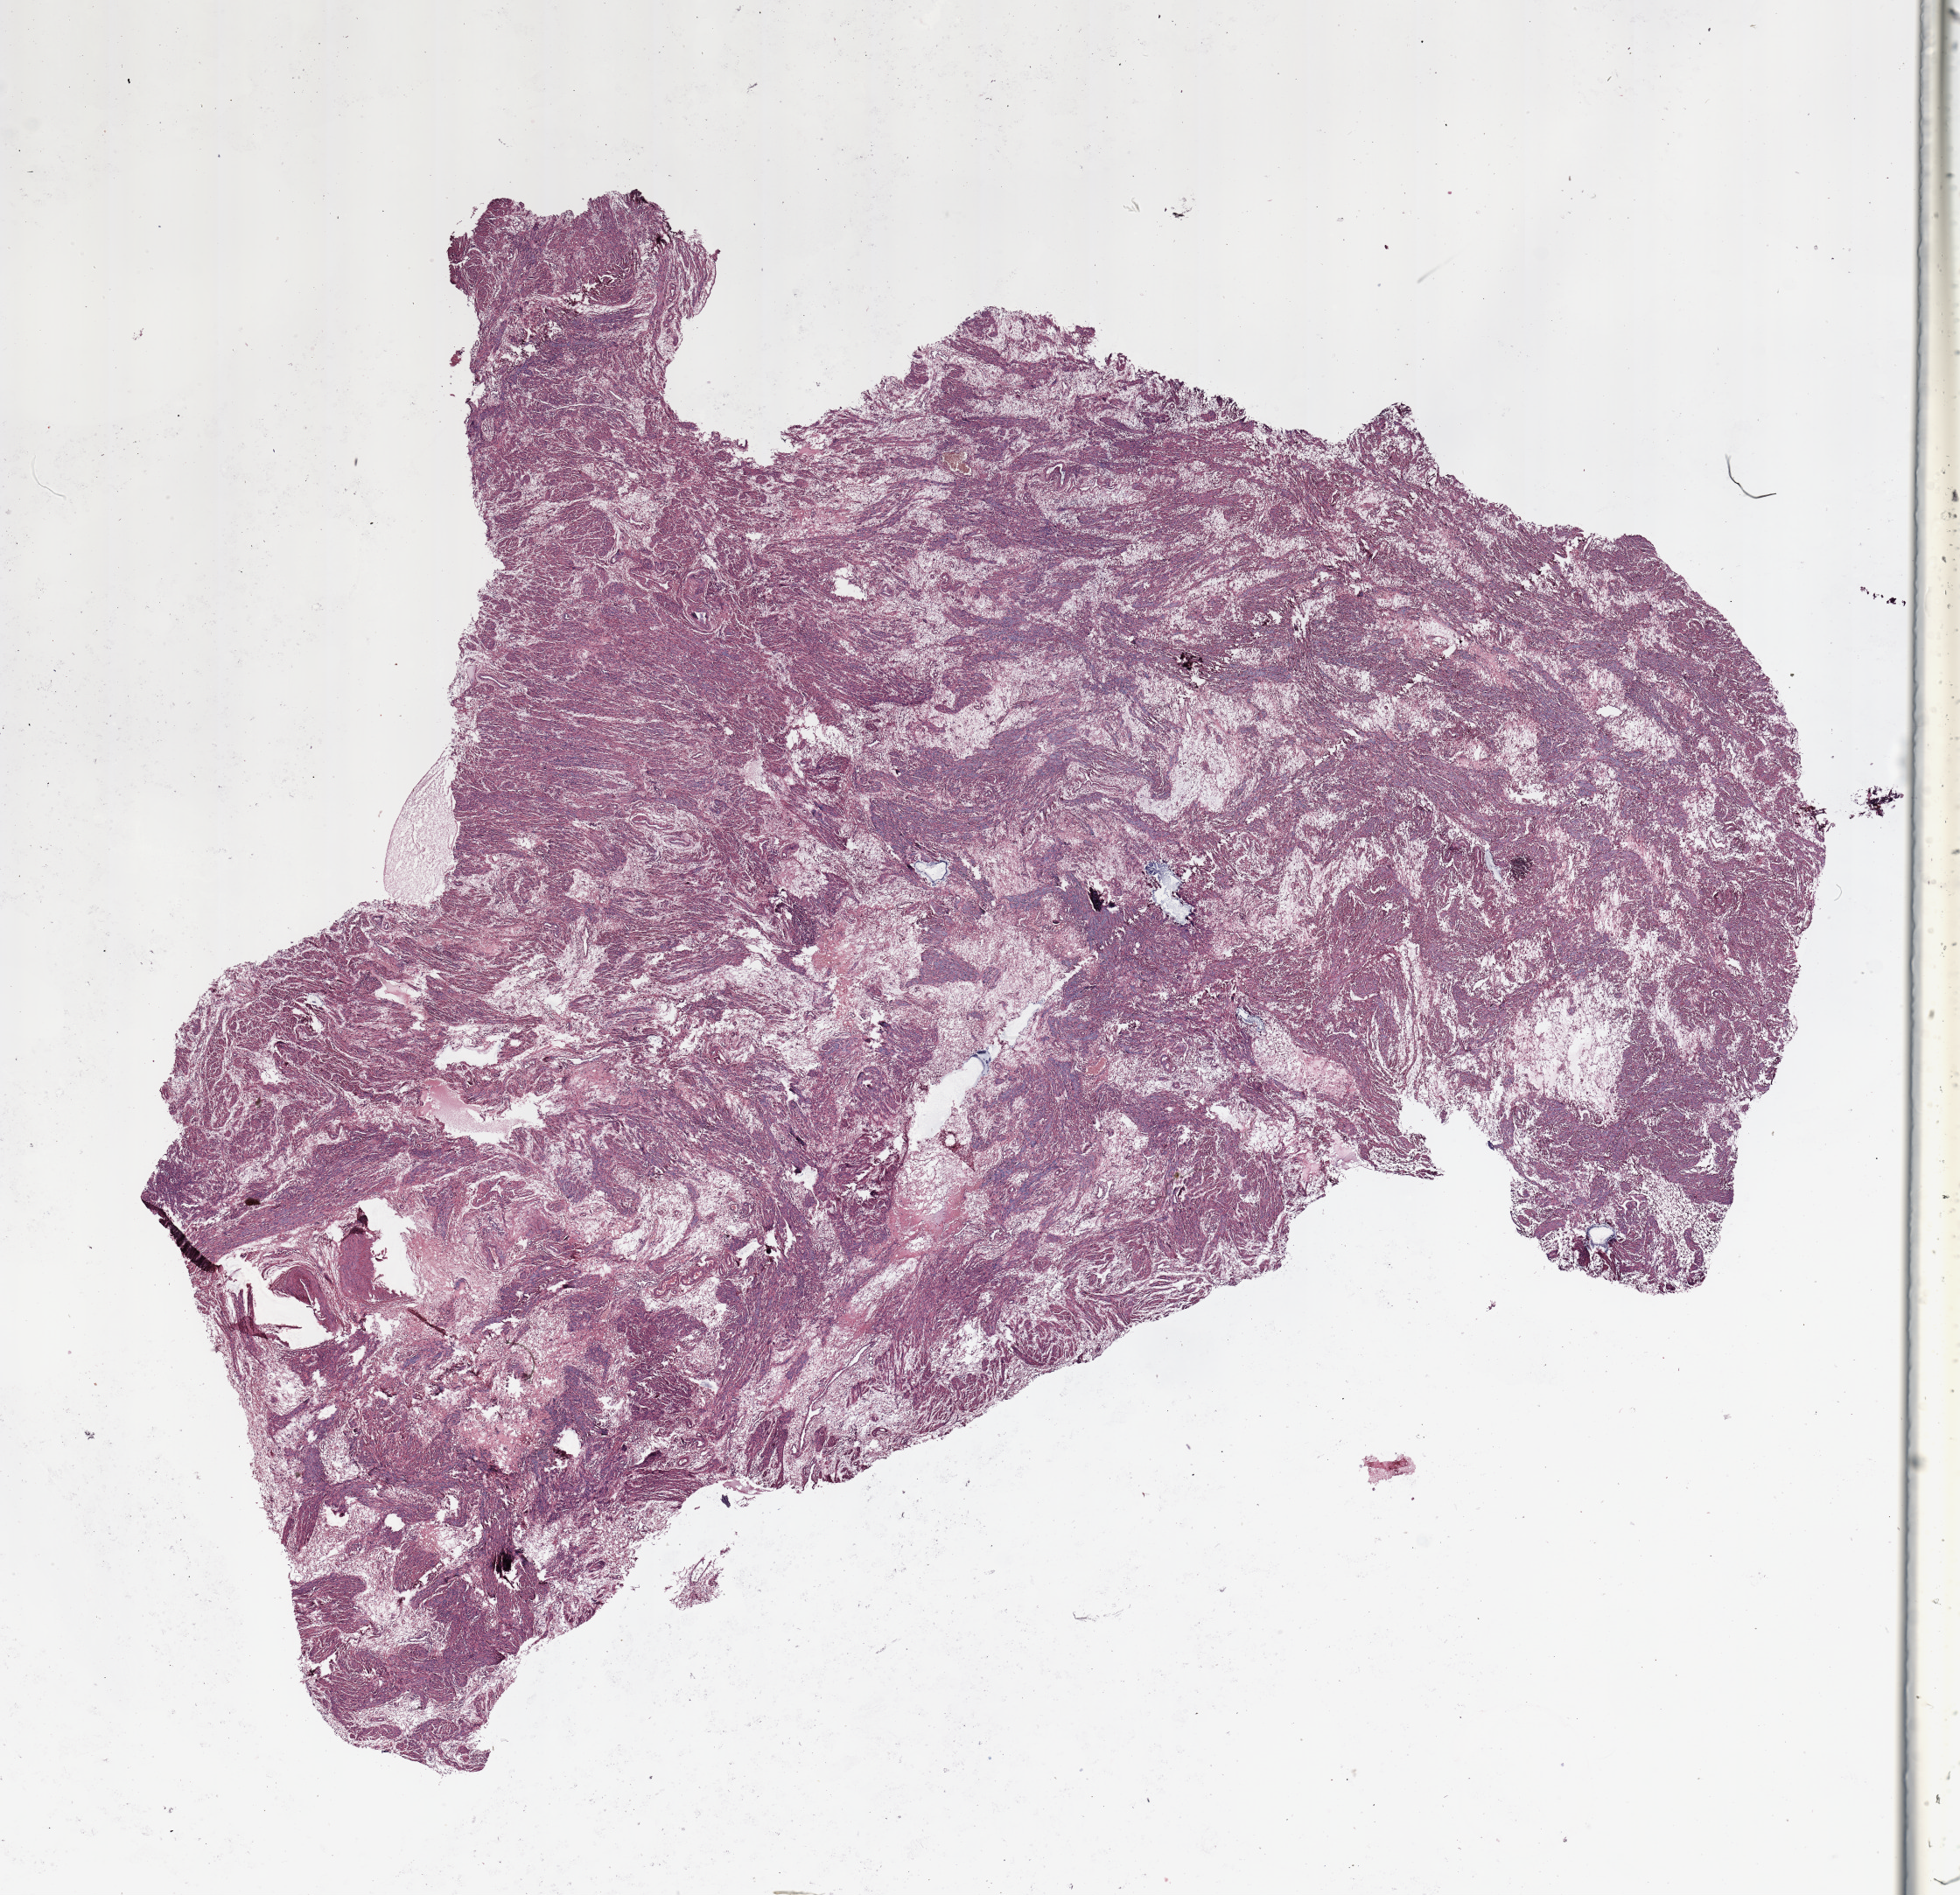
Whole-slide histology image, H&E, shown as a low-resolution overview of the whole scanned area (about 17.7 x 17.1 mm); normal (non-tumour) tissue sample, uterus. 59-year-old female patient.
- this section: normal (non-tumour) tissue from the same patient
- patient diagnosis: Endometrioid adenocarcinoma, NOS